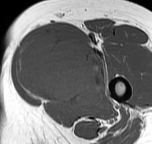
MRI of an extremity soft-tissue mass, one axial slice; slice 32 of 57 in the series (ordered by position); MR volume resampled by the dataset authors to the PET/CT grid (not the native acquisition matrix); 3.27 mm slice thickness; 152 × 144 image matrix, field of view 148 × 141 mm. Female patient. From the clinical record (not read from this slice): histological type: pleiomorphic leiomyosarcoma; grade: intermediate; site of the primary tumour: left thigh.
Structures marked on this image (expert contour drawn on MRI and transferred to this co-registered scan by the dataset authors):
- gross tumour volume including surrounding oedema: bounding box [x1, y1, x2, y2] px = [15, 35, 105, 107]
- gross tumour volume (mass): [15, 37, 105, 105]